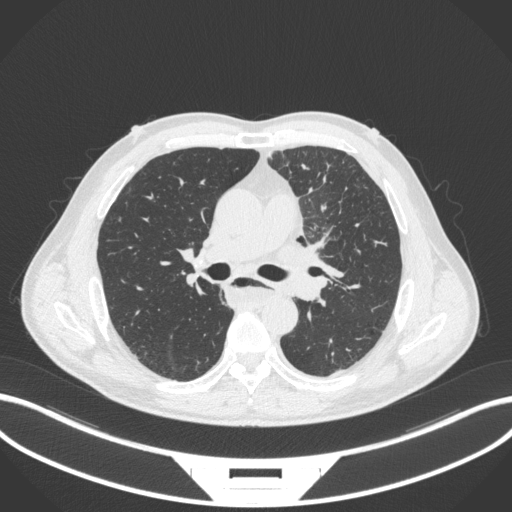
Chest CT, one axial slice; slice 228 of 411 in the series (ordered by position); reconstruction kernel B31f; lung window (W 1500 / L -600 HU); 512 × 512 image matrix, field of view 400 × 400 mm. Male patient, age 57 years. Case-level facts recorded for this patient, not image findings: clinical TNM (as recorded): T2a N1 M0.
Outlined on this slice (rectangle marked by the reading radiologist):
- lung tumour (recorded histology: squamous cell carcinoma): bounding box <273,230,338,278> (left, top, right, bottom; pixels)